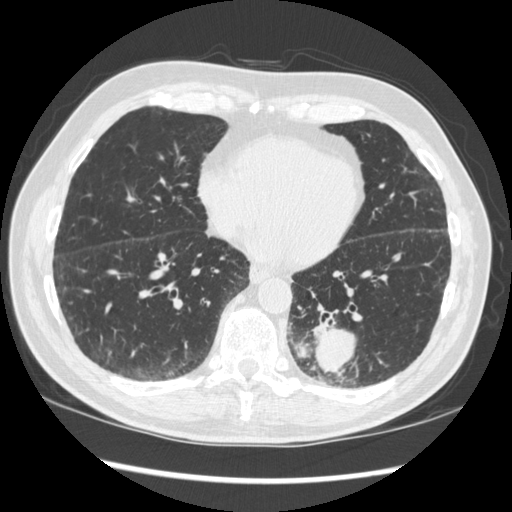
Chest CT (low-dose screening protocol), one axial image. Baseline annual screen. Lung window (W 1500 / L -600 HU). 1.25 mm slice thickness. Slice 119 of 348 in the series. 512 × 512 image matrix, field of view 360 × 360 mm. Male, age 72 years at enrolment.
Expert-annotated lung lesion, bounding box <274,296,378,384> (left, top, right, bottom; pixels). The screening reader recorded 2 non-calcified nodules or masses ≥4 mm on this exam (left lower lobe, right middle lobe); which of them this box marks is not recorded.